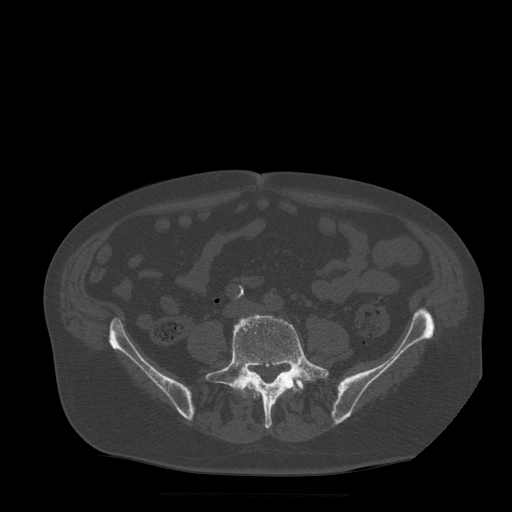
CT including the spine, one axial slice. Slice 91 of 522 in the series (ordered by position). Bone window (W 1800 / L 400 HU). 512 × 512 image matrix, field of view 420 × 420 mm. Patient age 72 years. Case-level facts recorded for this patient, not image findings: primary cancer: prostate.
Outlined on this slice (semi-automatic segmentation, software-assisted and operator-edited):
- L5 vertebra: bounding box (x1, y1, x2, y2) in pixels: (205, 314, 329, 429)